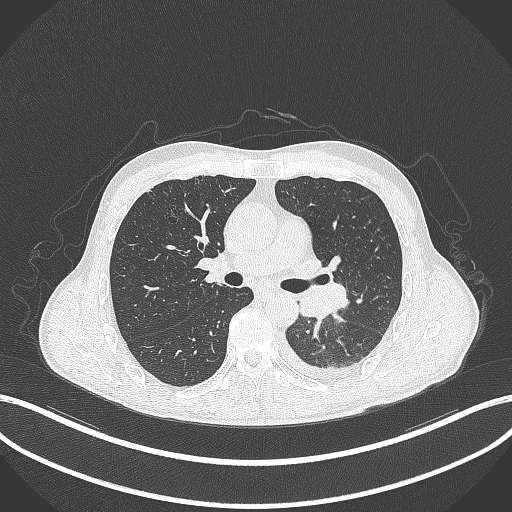
Chest CT, one axial slice; position 192 of 295 along the scan axis; reconstruction kernel B70f; 120 kVp; lung window (W 1500 / L -600 HU); 1 mm slice thickness; 512 × 512 image matrix, field of view 400 × 400 mm. Patient: male, 47 years. Case-level facts recorded for this patient, not image findings: clinical TNM (as recorded): T3 N1 M1c; histopathological grade: G3.
Outlined on this slice (rectangle marked by the reading radiologist):
- lung tumour (recorded histology: small cell carcinoma): bounding box <295,281,352,319> (left, top, right, bottom; pixels)